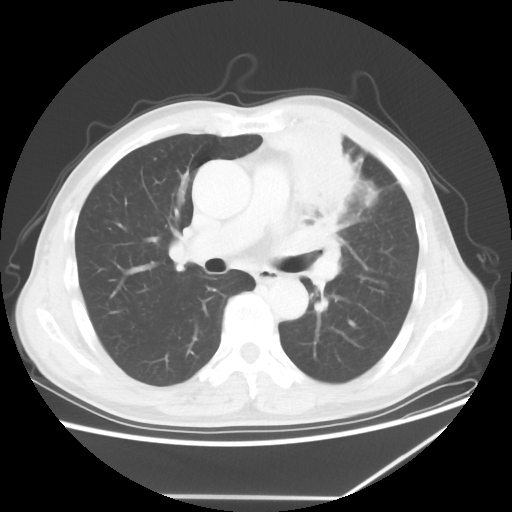
Chest CT, one axial slice; reconstruction kernel STANDARD; 100 kVp; lung window (W 1500 / L -600 HU); 5 mm slice thickness; 512 × 512 image matrix, field of view 383 × 383 mm. Male patient, age 64 years. From the clinical record (not read from this slice): clinical TNM (as recorded): T1c N1 M1; histopathological grade: G2.
Annotated regions visible in this slice (bounding box drawn by a radiologist):
- lung tumour (recorded histology: squamous cell carcinoma): bounding box [x1, y1, x2, y2] px = [276, 130, 367, 219]